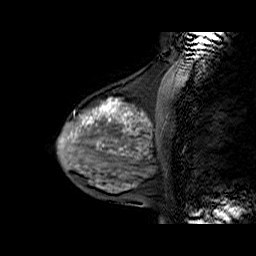
Breast MRI (dynamic contrast-enhanced), one sagittal slice. Position 22 of 60 along the scan axis. Dynamic contrast-enhanced series, time point 2 of 6 at this slice position (early post-contrast). 1.5 T. TE 6.3 ms, TR 32.9 ms. 4 mm slice thickness. 256 × 256 image matrix. Female patient. Case-level facts recorded for this patient, not image findings: setting: breast cancer imaged before/during neoadjuvant chemotherapy; receptor status: HR-positive, HER2-negative.
Annotated regions visible in this slice (semi-automatically segmented with operator editing):
- analysis volume of interest (the breast-tissue region the enhancement analysis was run in; not a lesion): bounding box <58,86,169,170> (left, top, right, bottom; pixels)
- tumour enhancement mask (voxels above the 100 % enhancement threshold inside the analysis volume of interest): <83,99,149,125>